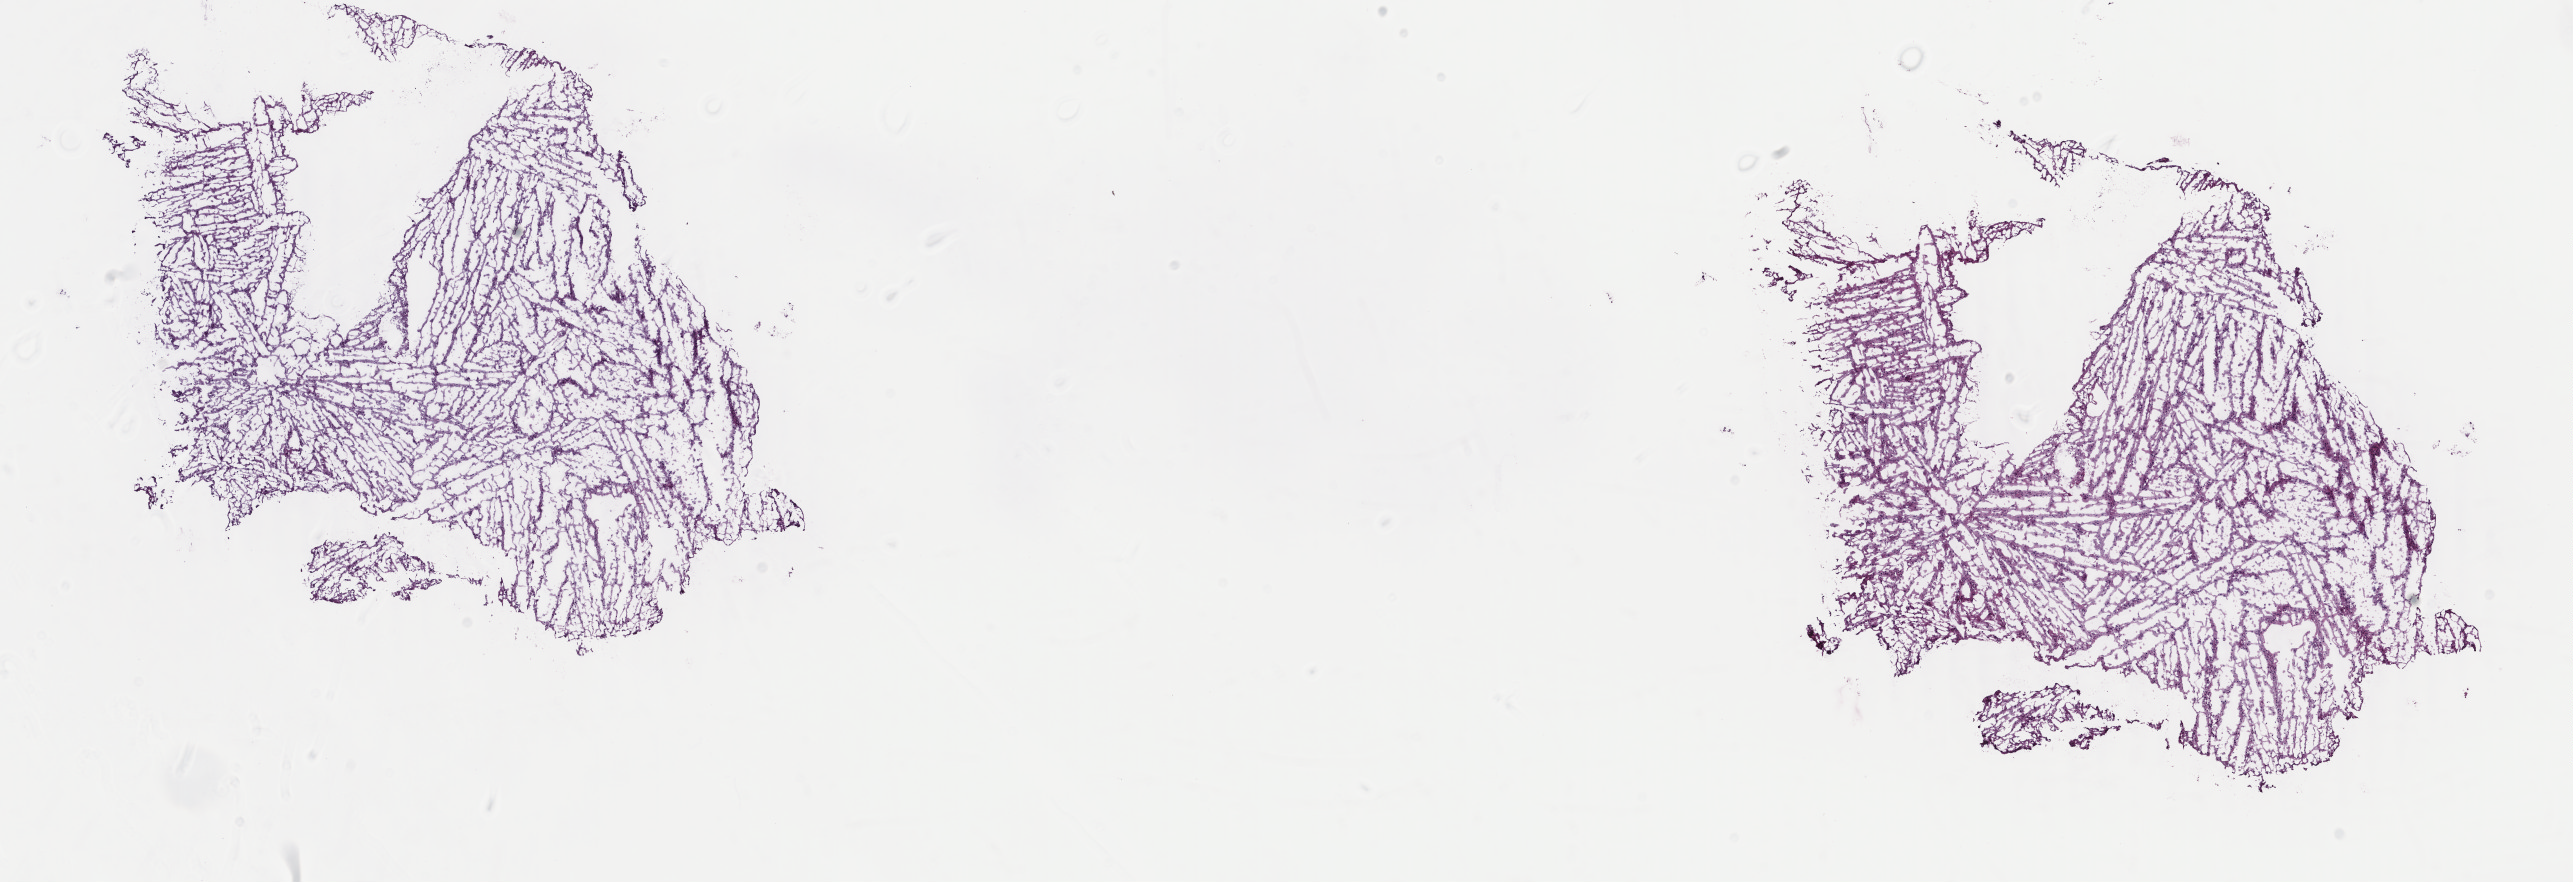
Digitized Hematoxylin and eosin (H&E) stained tissue section (whole slide), low-resolution overview of the scanned area, about 20.5 x 7.0 mm. Frozen section from the top of the tissue portion. Primary tumour sample from the brain. Female, age 20 years at initial diagnosis. Histologic grade: G2 (moderately differentiated). Pathologist review of this section (percent, as recorded): tumour cells 45%, tumour nuclei 75%, normal cells 10%, stromal cells 45%, necrosis 0%. Infiltration values recorded for this section: lymphocyte infiltration 0%, monocyte infiltration 0%, neutrophil infiltration 0%.
- laterality: right
- diagnosis: Astrocytoma, NOS (cerebrum)